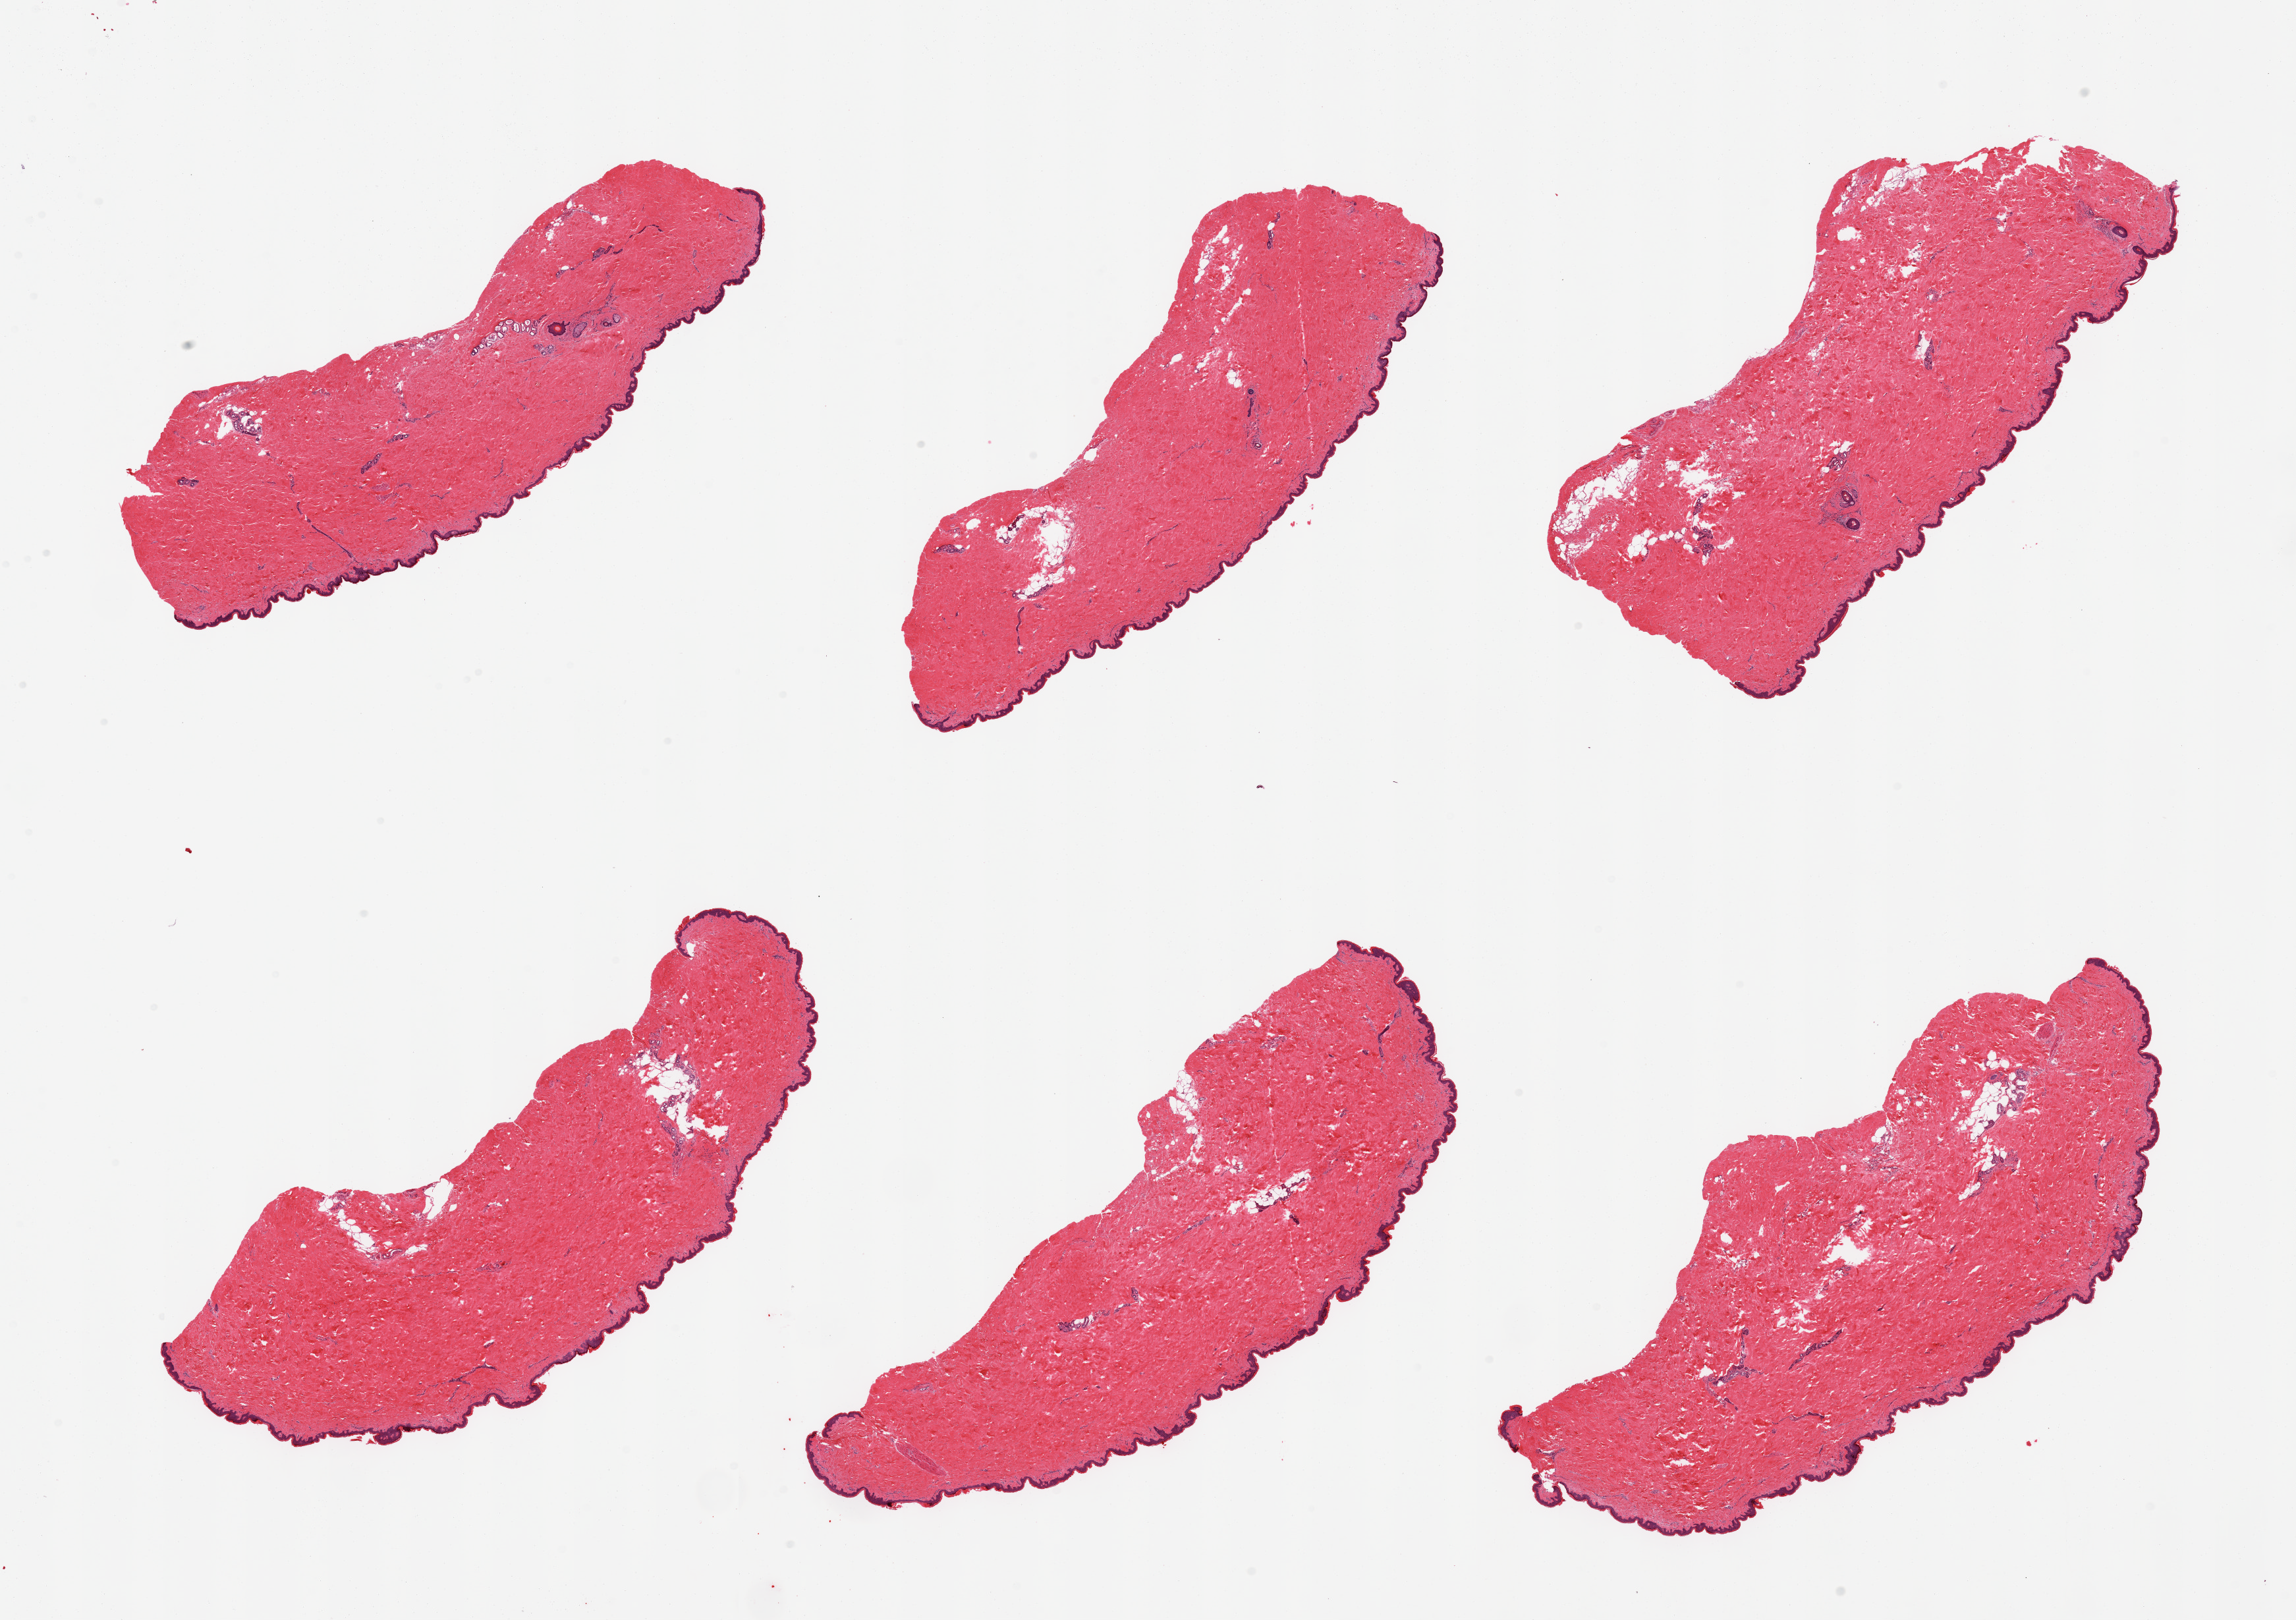
Whole-slide image, hematoxylin and eosin (H&E) stain, shown as a low-resolution overview of the whole scanned area (about 27.6 x 19.4 mm), PAXgene-fixed, paraffin-embedded tissue, target tissue: skin of suprapubic region, tissue donor sample. Donor: female.
Review note (as recorded): 6 pieces, well trimmed.